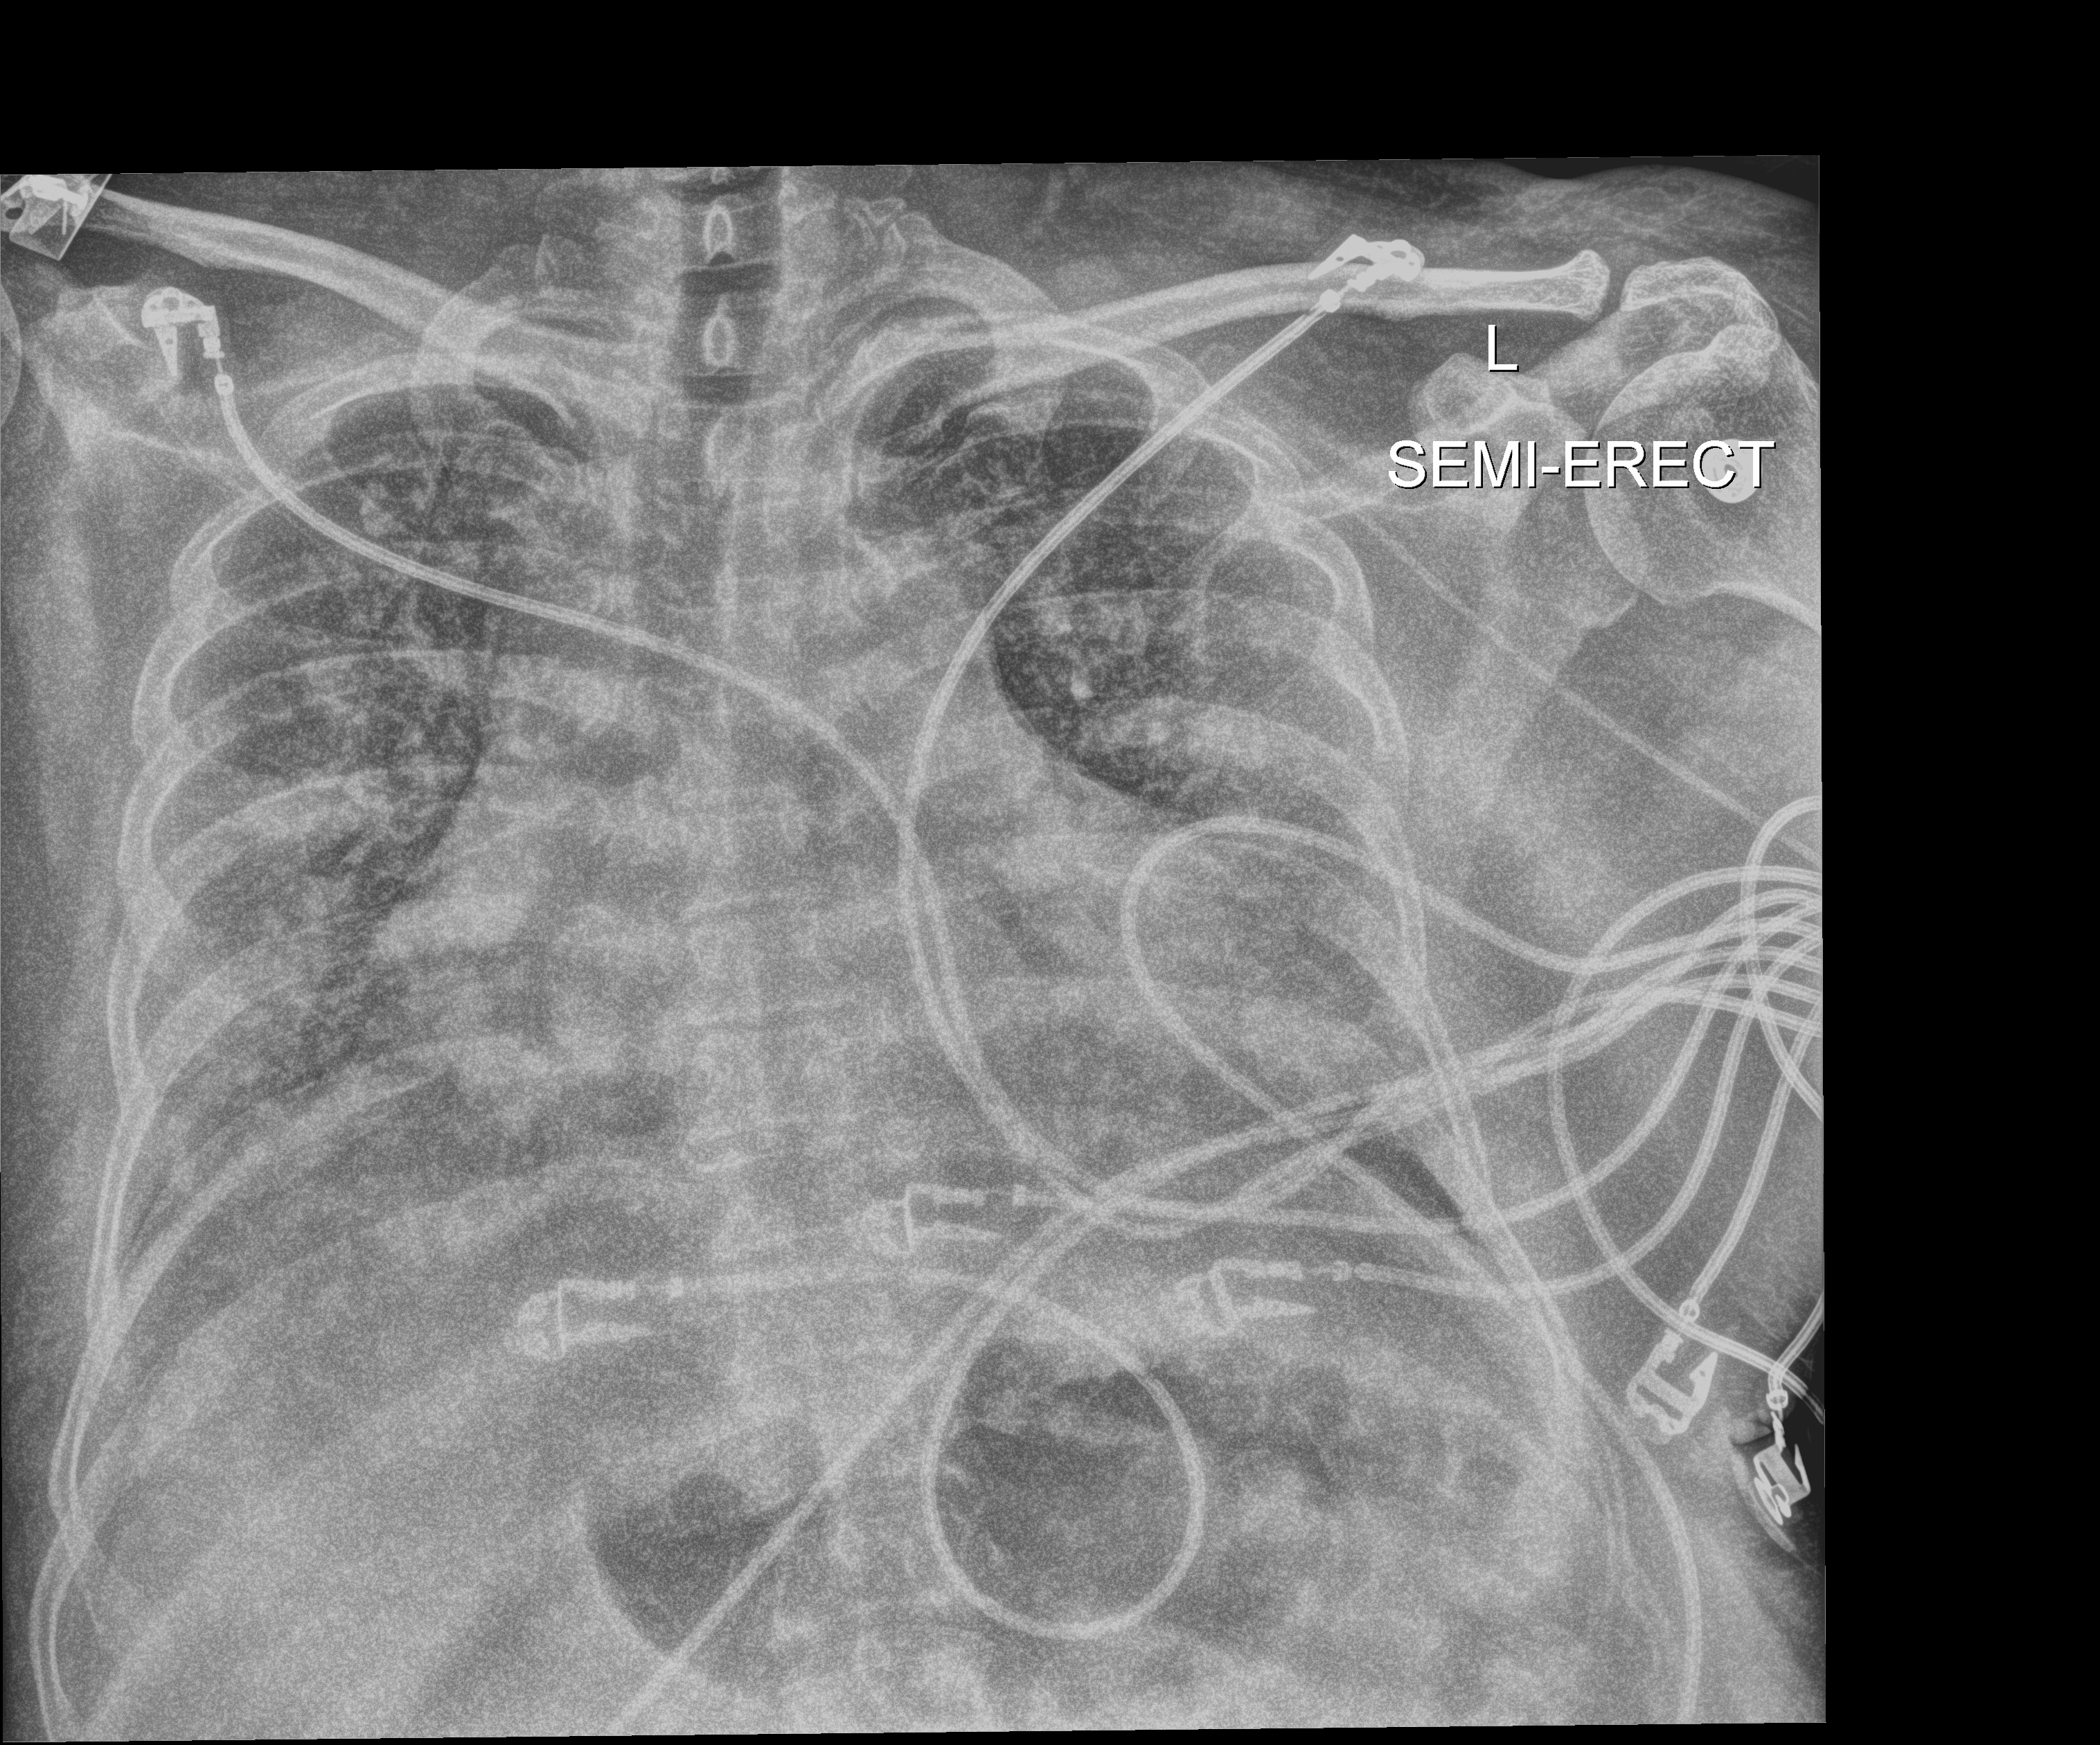
Portable chest radiograph. Adult patient hospitalised with COVID-19, age 18–59 years.
From the hospital-stay record, not from the radiograph (when in the stay this image was taken is not recorded):
- admitted to intensive care during this hospital stay: yes